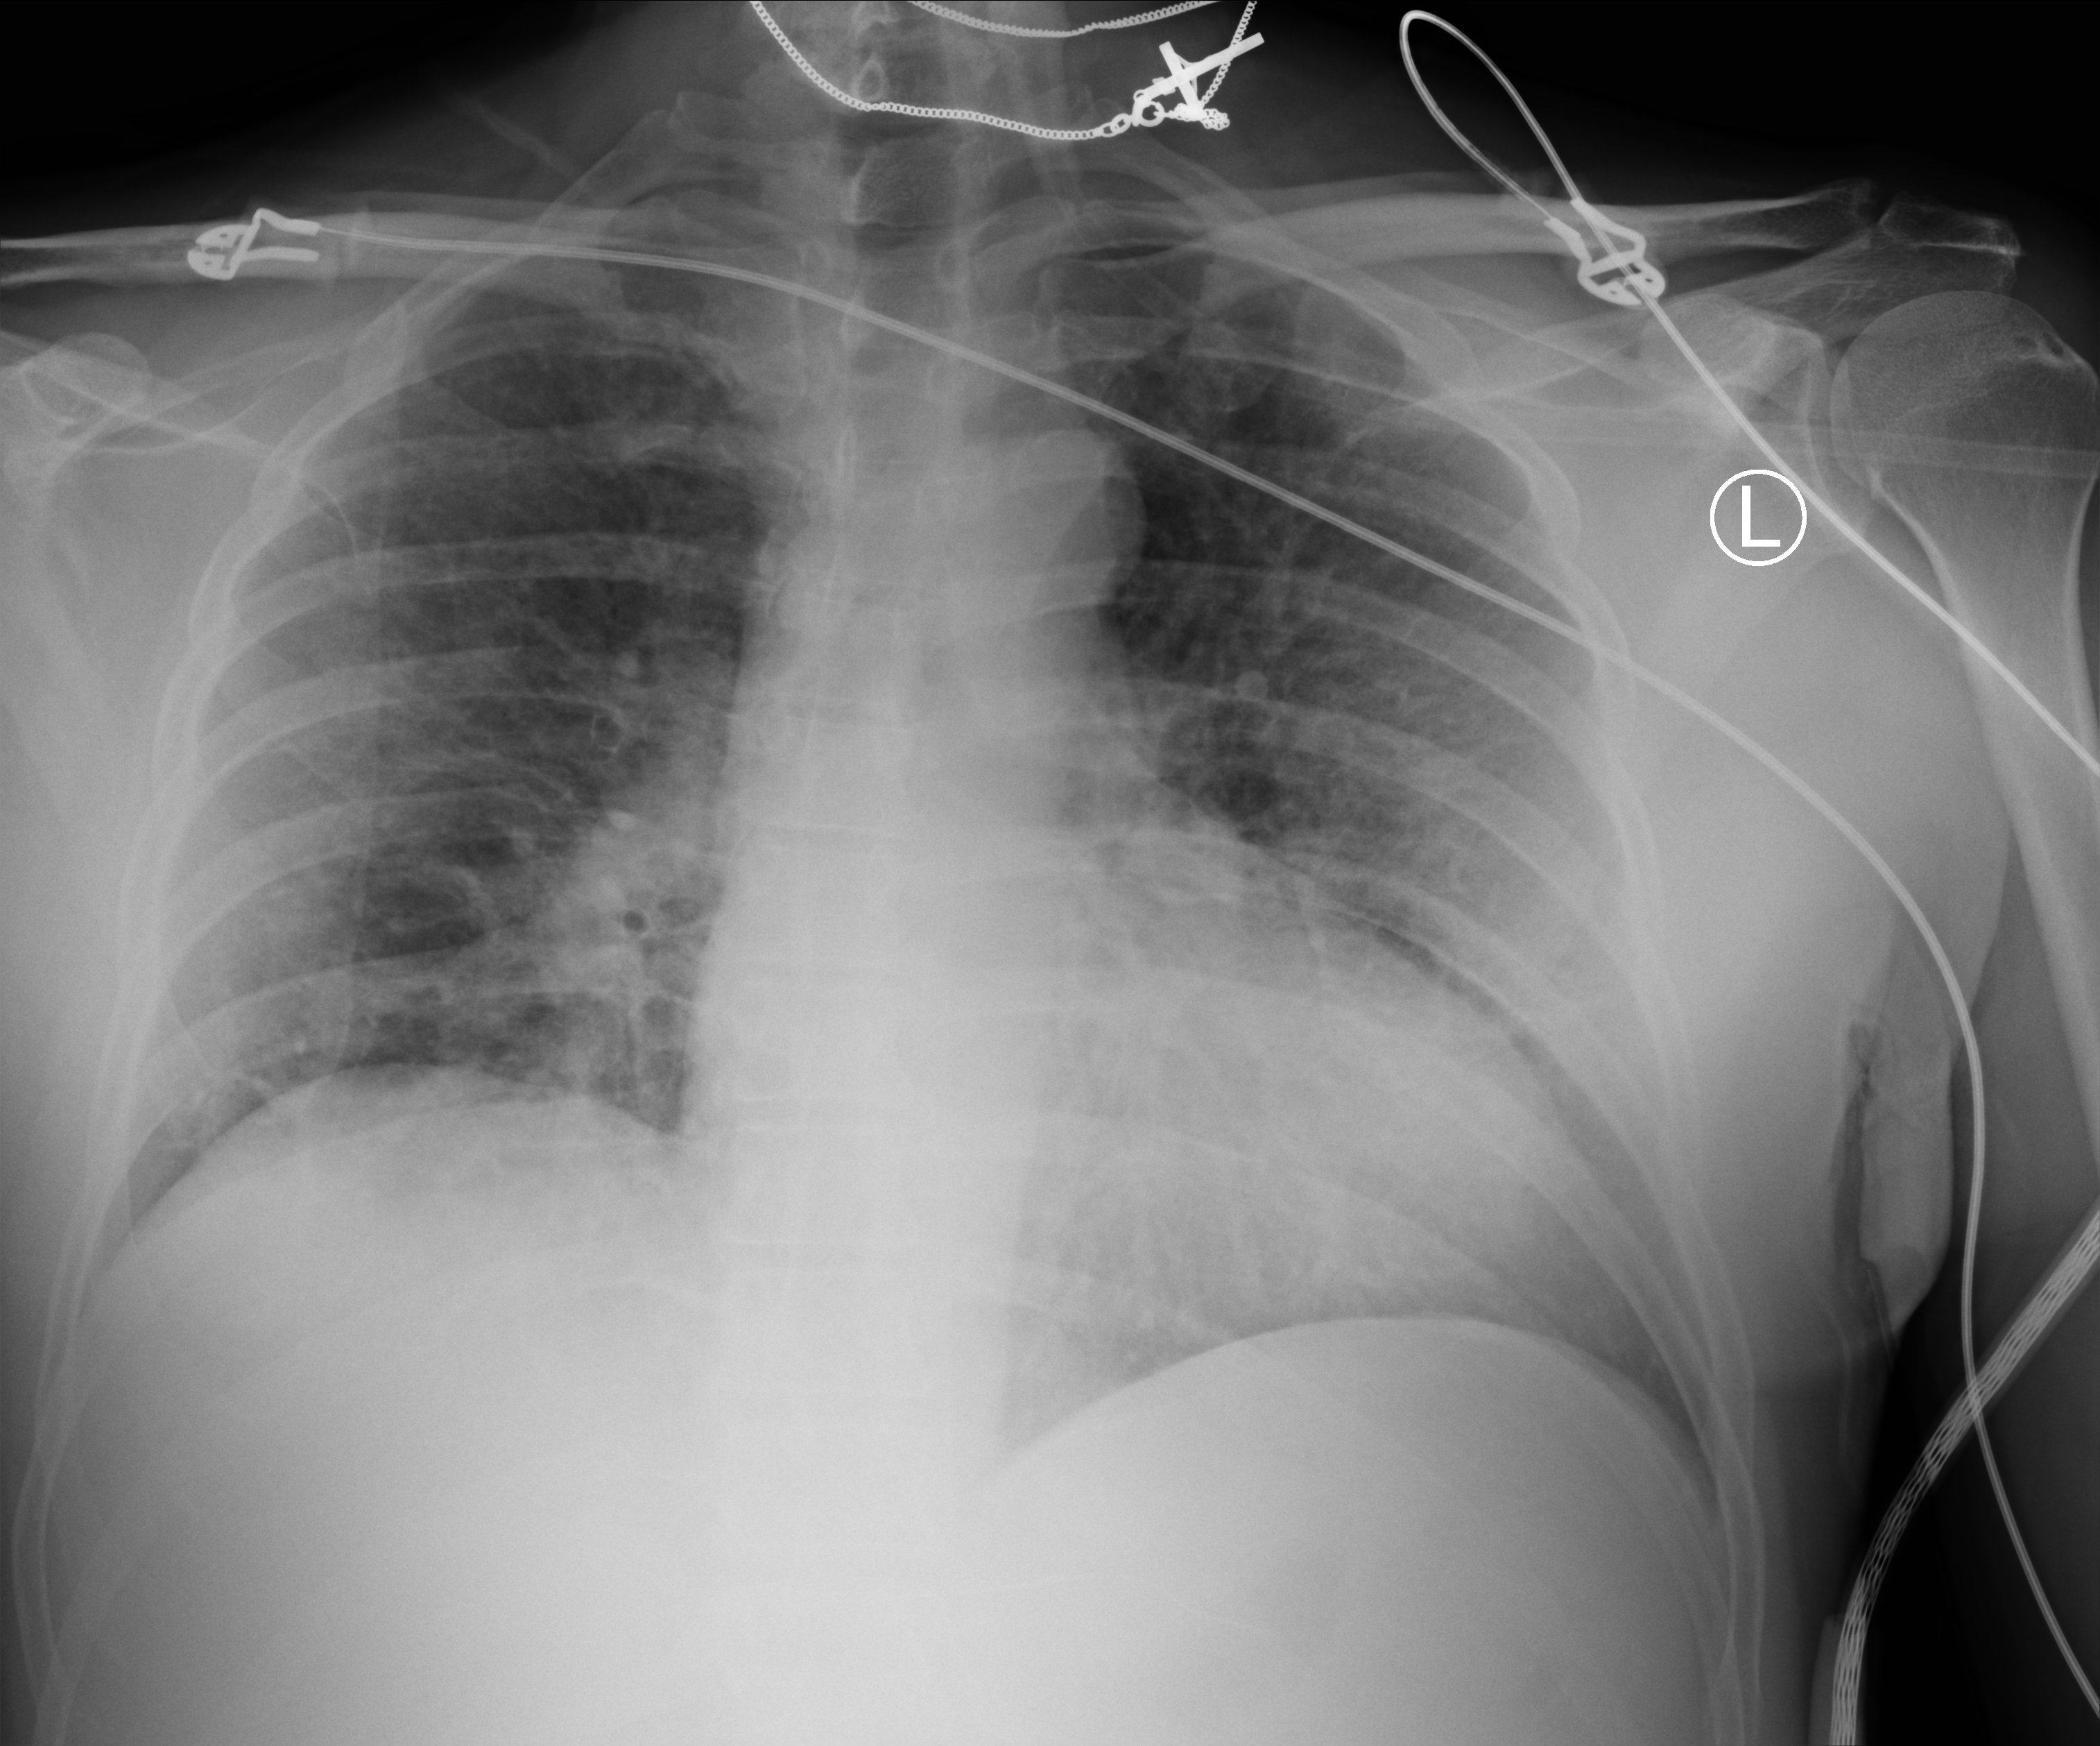
Bedside chest radiograph (computed radiography); anteroposterior (AP) projection. Patient hospitalised with COVID-19; male, aged 60–74 years.
Admission-level facts for this patient (not findings on this image; timing relative to this image not recorded):
- mechanically ventilated during this hospital stay: no